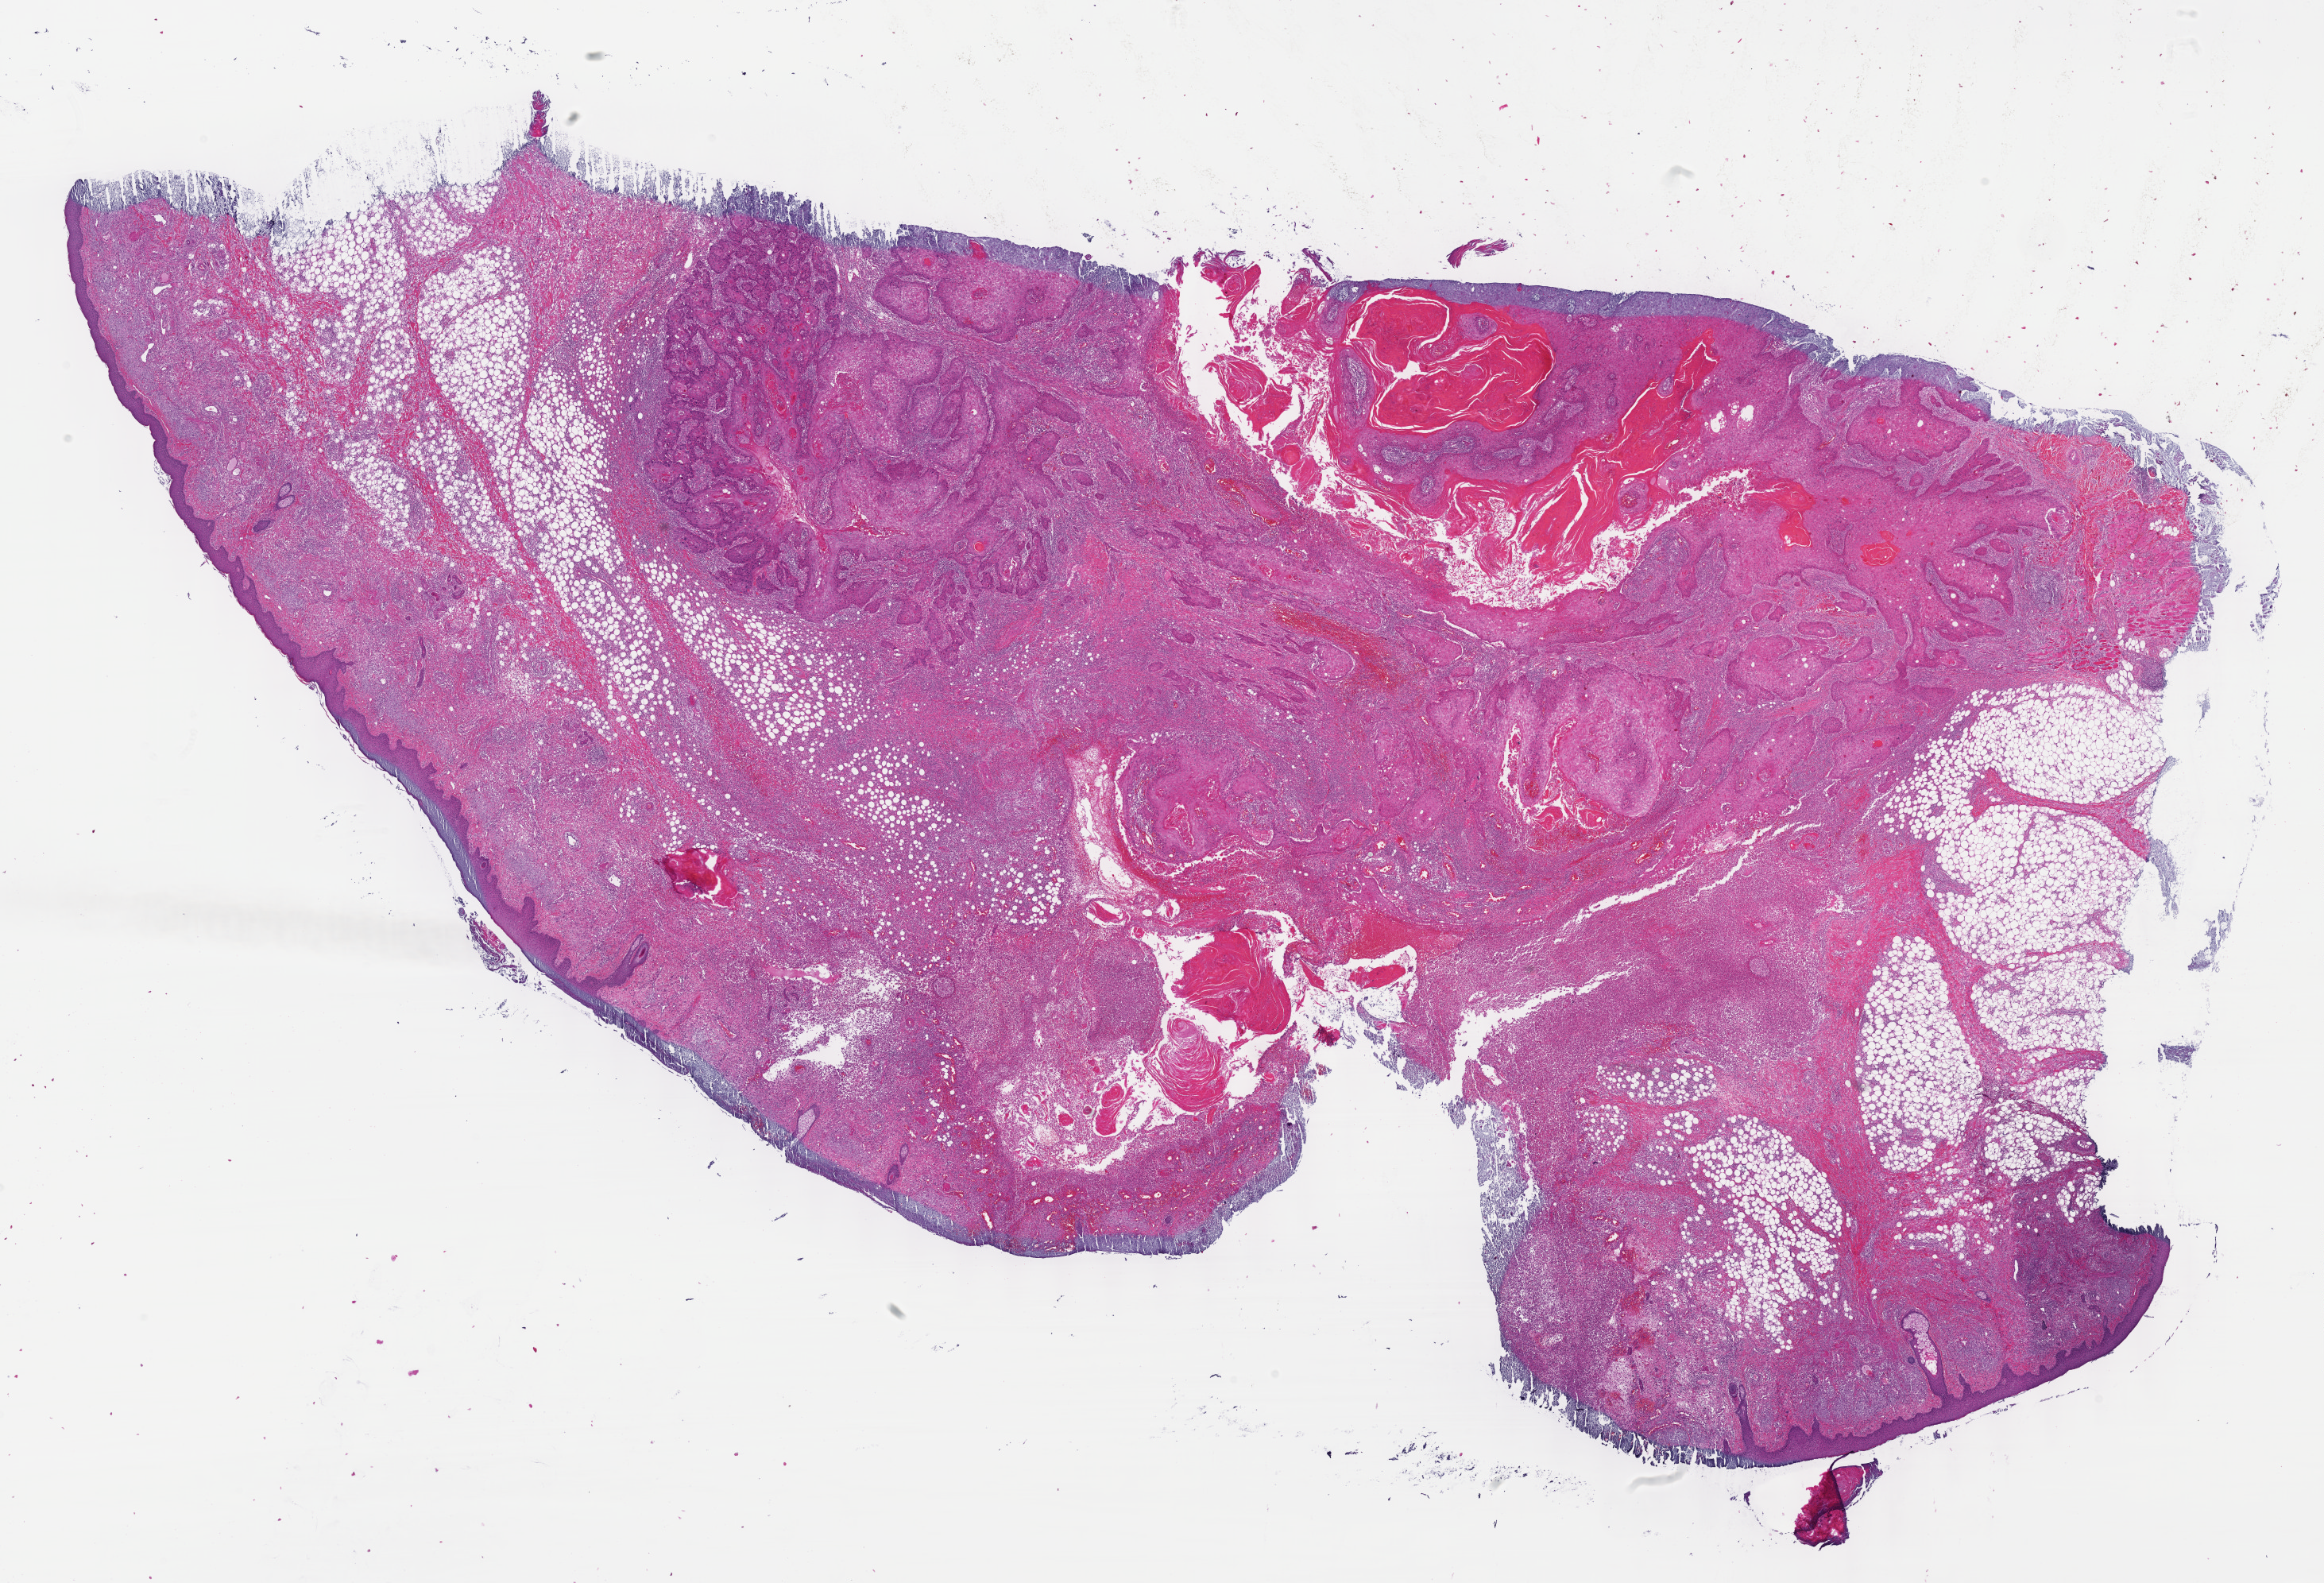
Hematoxylin and eosin (H&E) stained whole-slide image, shown as a low-resolution overview of the whole scanned area (about 23.6 x 16.1 mm); FFPE section; head and neck, primary tumour sample. Female, age 74 years at initial diagnosis. Histologic grade: G2 (moderately differentiated).
* laterality: right
* AJCC pathologic stage: II (7th edition)
* pathologic diagnosis: Squamous cell carcinoma, NOS (overlapping lesion of lip, oral cavity and pharynx)